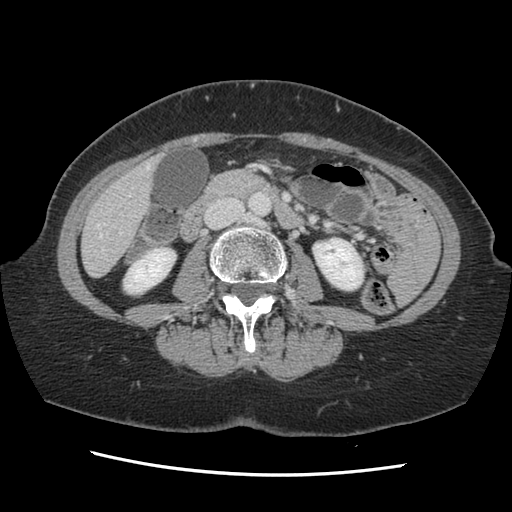
Contrast-enhanced abdominal CT, one axial slice; slice 40 of 141 in the series (ordered by position); soft-tissue window (W 400 / L 40 HU); 512 × 512 image matrix, field of view 330 × 330 mm. Female patient, age 61 years. Case-level facts recorded for this patient, not image findings: diagnosis: colorectal cancer liver metastases, imaged before liver resection; multiple liver metastases: no; largest metastasis: 2.4 cm; disease in both lobes: no.
Structures marked on this image (outlined manually by an expert reader):
- hepatic veins: bounding box [x1, y1, x2, y2] px = [97, 163, 150, 237]
- liver: [83, 161, 157, 277]
- planned liver remnant (the part of the liver to remain after resection): [83, 168, 154, 277]